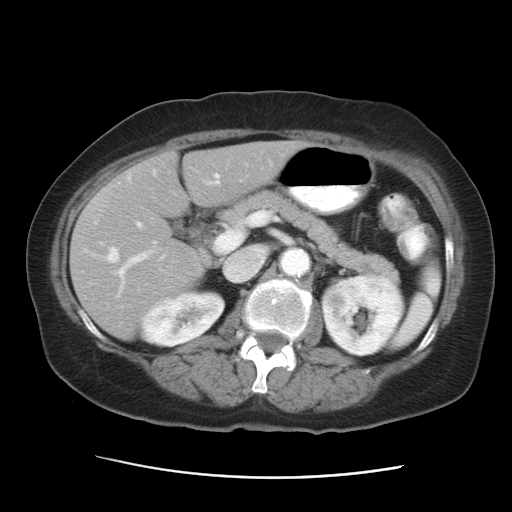
Contrast-enhanced abdominal CT, one axial slice; position 15 of 29 along the scan axis; reconstruction kernel STANDARD; 120 kVp; soft-tissue window (W 400 / L 40 HU); 512 × 512 image matrix, field of view 354 × 354 mm. Female patient, age 64 years. Case-level facts recorded for this patient, not image findings: diagnosis: colorectal cancer liver metastases, imaged before liver resection; multiple liver metastases: no; largest metastasis: 2.5 cm; disease in both lobes: no.
Annotated regions visible in this slice (manually delineated by an expert):
- hepatic veins: box from (x=106, y=175) to (x=219, y=263) px
- liver: (x=71, y=141)–(x=303, y=339)
- planned liver remnant (the part of the liver to remain after resection): (x=70, y=141)–(x=303, y=325)
- portal vein (with intrahepatic branches): (x=115, y=182)–(x=237, y=290)